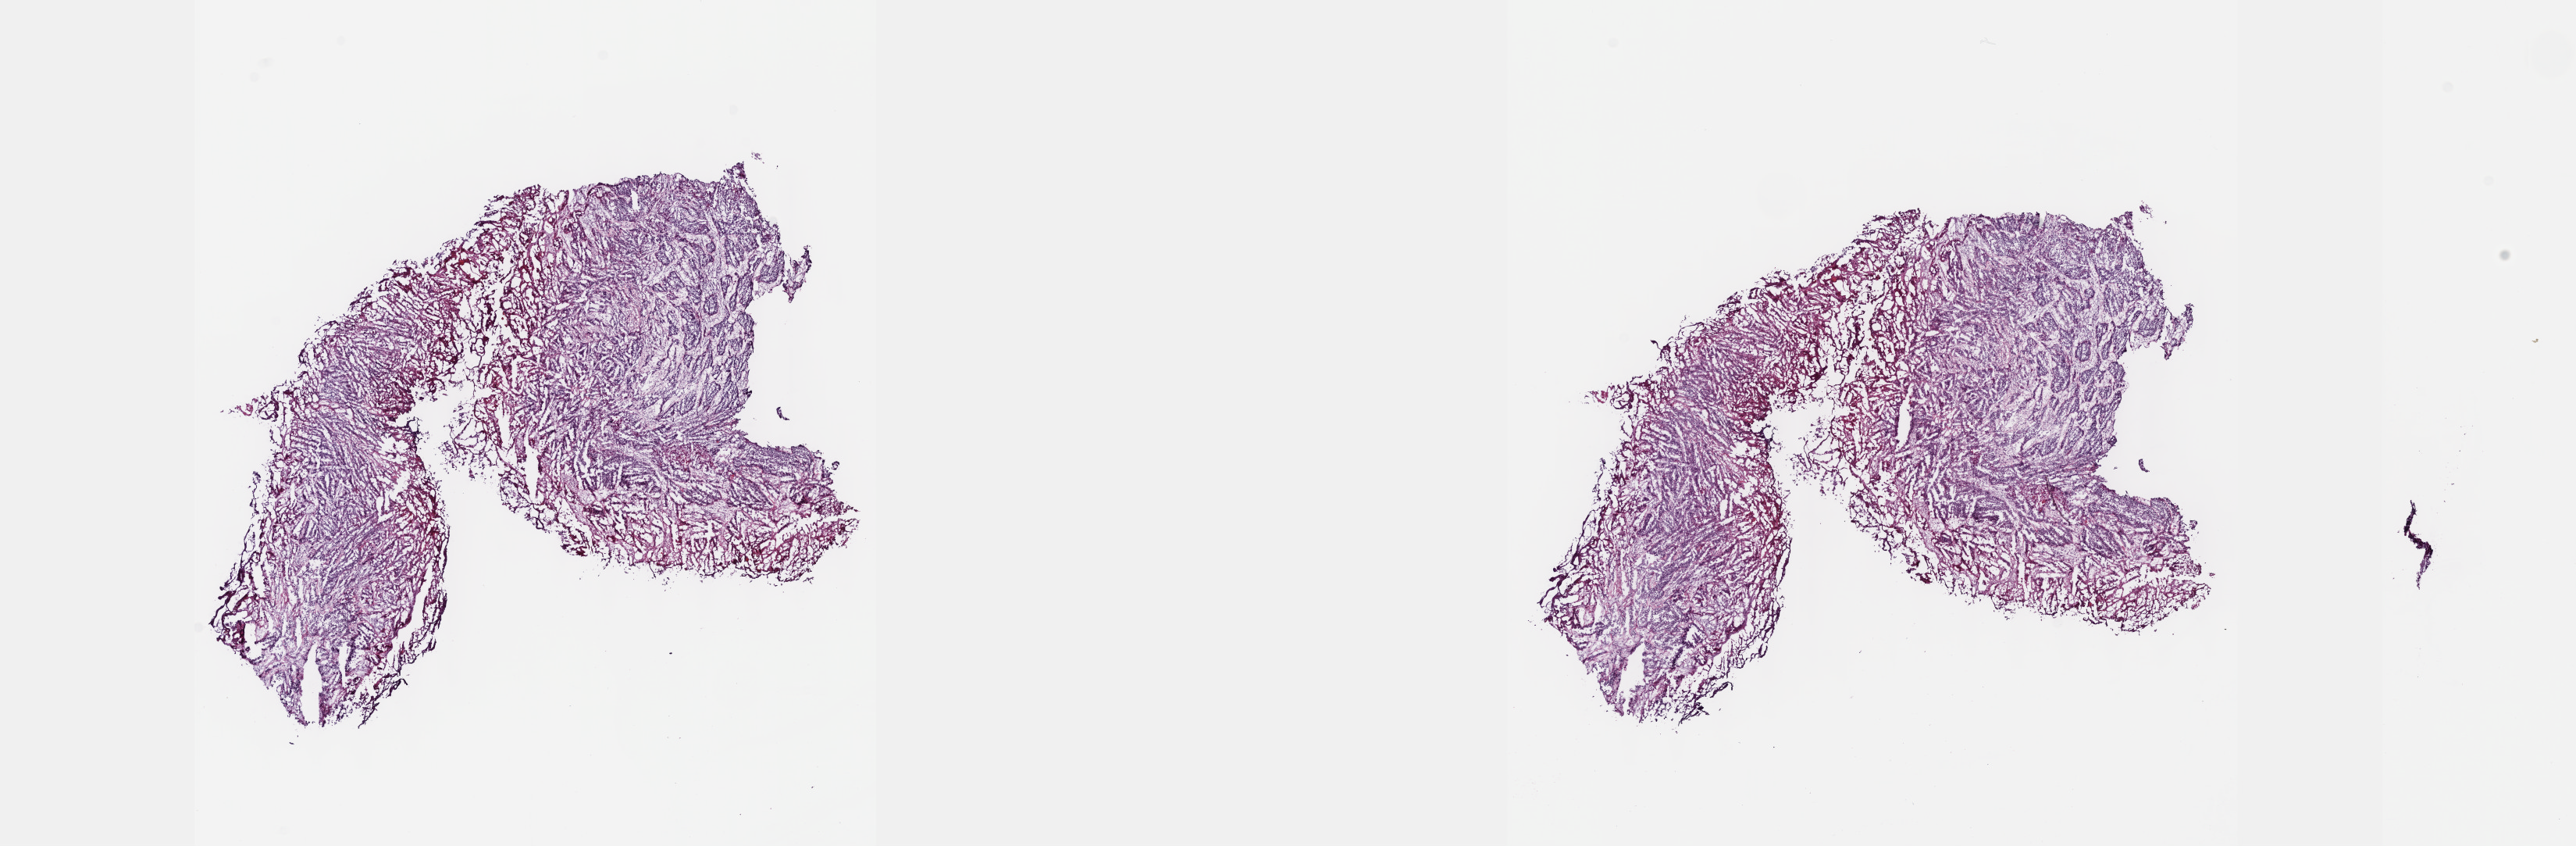
Hematoxylin and eosin (H&E) stained whole-slide image — low-resolution overview of the scanned area, about 26.7 x 8.8 mm (acquisition: 40x scan); frozen section from the top of the tissue portion; primary tumour sample from the bladder. Patient: female, age at initial diagnosis 78 years. Histologic grade: high grade. Slide review estimates, as recorded: tumour cells 100%, tumour nuclei 75%, normal cells 0%, stromal cells 0%, necrosis 0%. Infiltration values recorded for this section: lymphocyte infiltration 3%, monocyte infiltration 0%, neutrophil infiltration 0%.
Diagnosis: Transitional cell carcinoma. AJCC pathologic stage: II (7th edition).